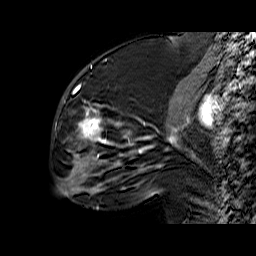
Breast MRI (dynamic contrast-enhanced), one sagittal slice. Slice 26 of 60 in the series (ordered by position). Dynamic contrast-enhanced series, time point 2 of 6 at this slice position (early post-contrast). 1.5 T. TE 6.4 ms, TR 32.9 ms. 256 × 256 image matrix, field of view 200 × 200 mm. Female patient. Case-level facts recorded for this patient, not image findings: setting: breast cancer imaged before/during neoadjuvant chemotherapy; receptor status: triple-negative.
Outlined on this slice (semi-automatically segmented with operator editing):
- analysis volume of interest (the breast-tissue region the enhancement analysis was run in; not a lesion): bounding box <57,65,159,174> (left, top, right, bottom; pixels)
- tumour enhancement mask (voxels above the 100 % enhancement threshold inside the analysis volume of interest): <72,86,159,171>